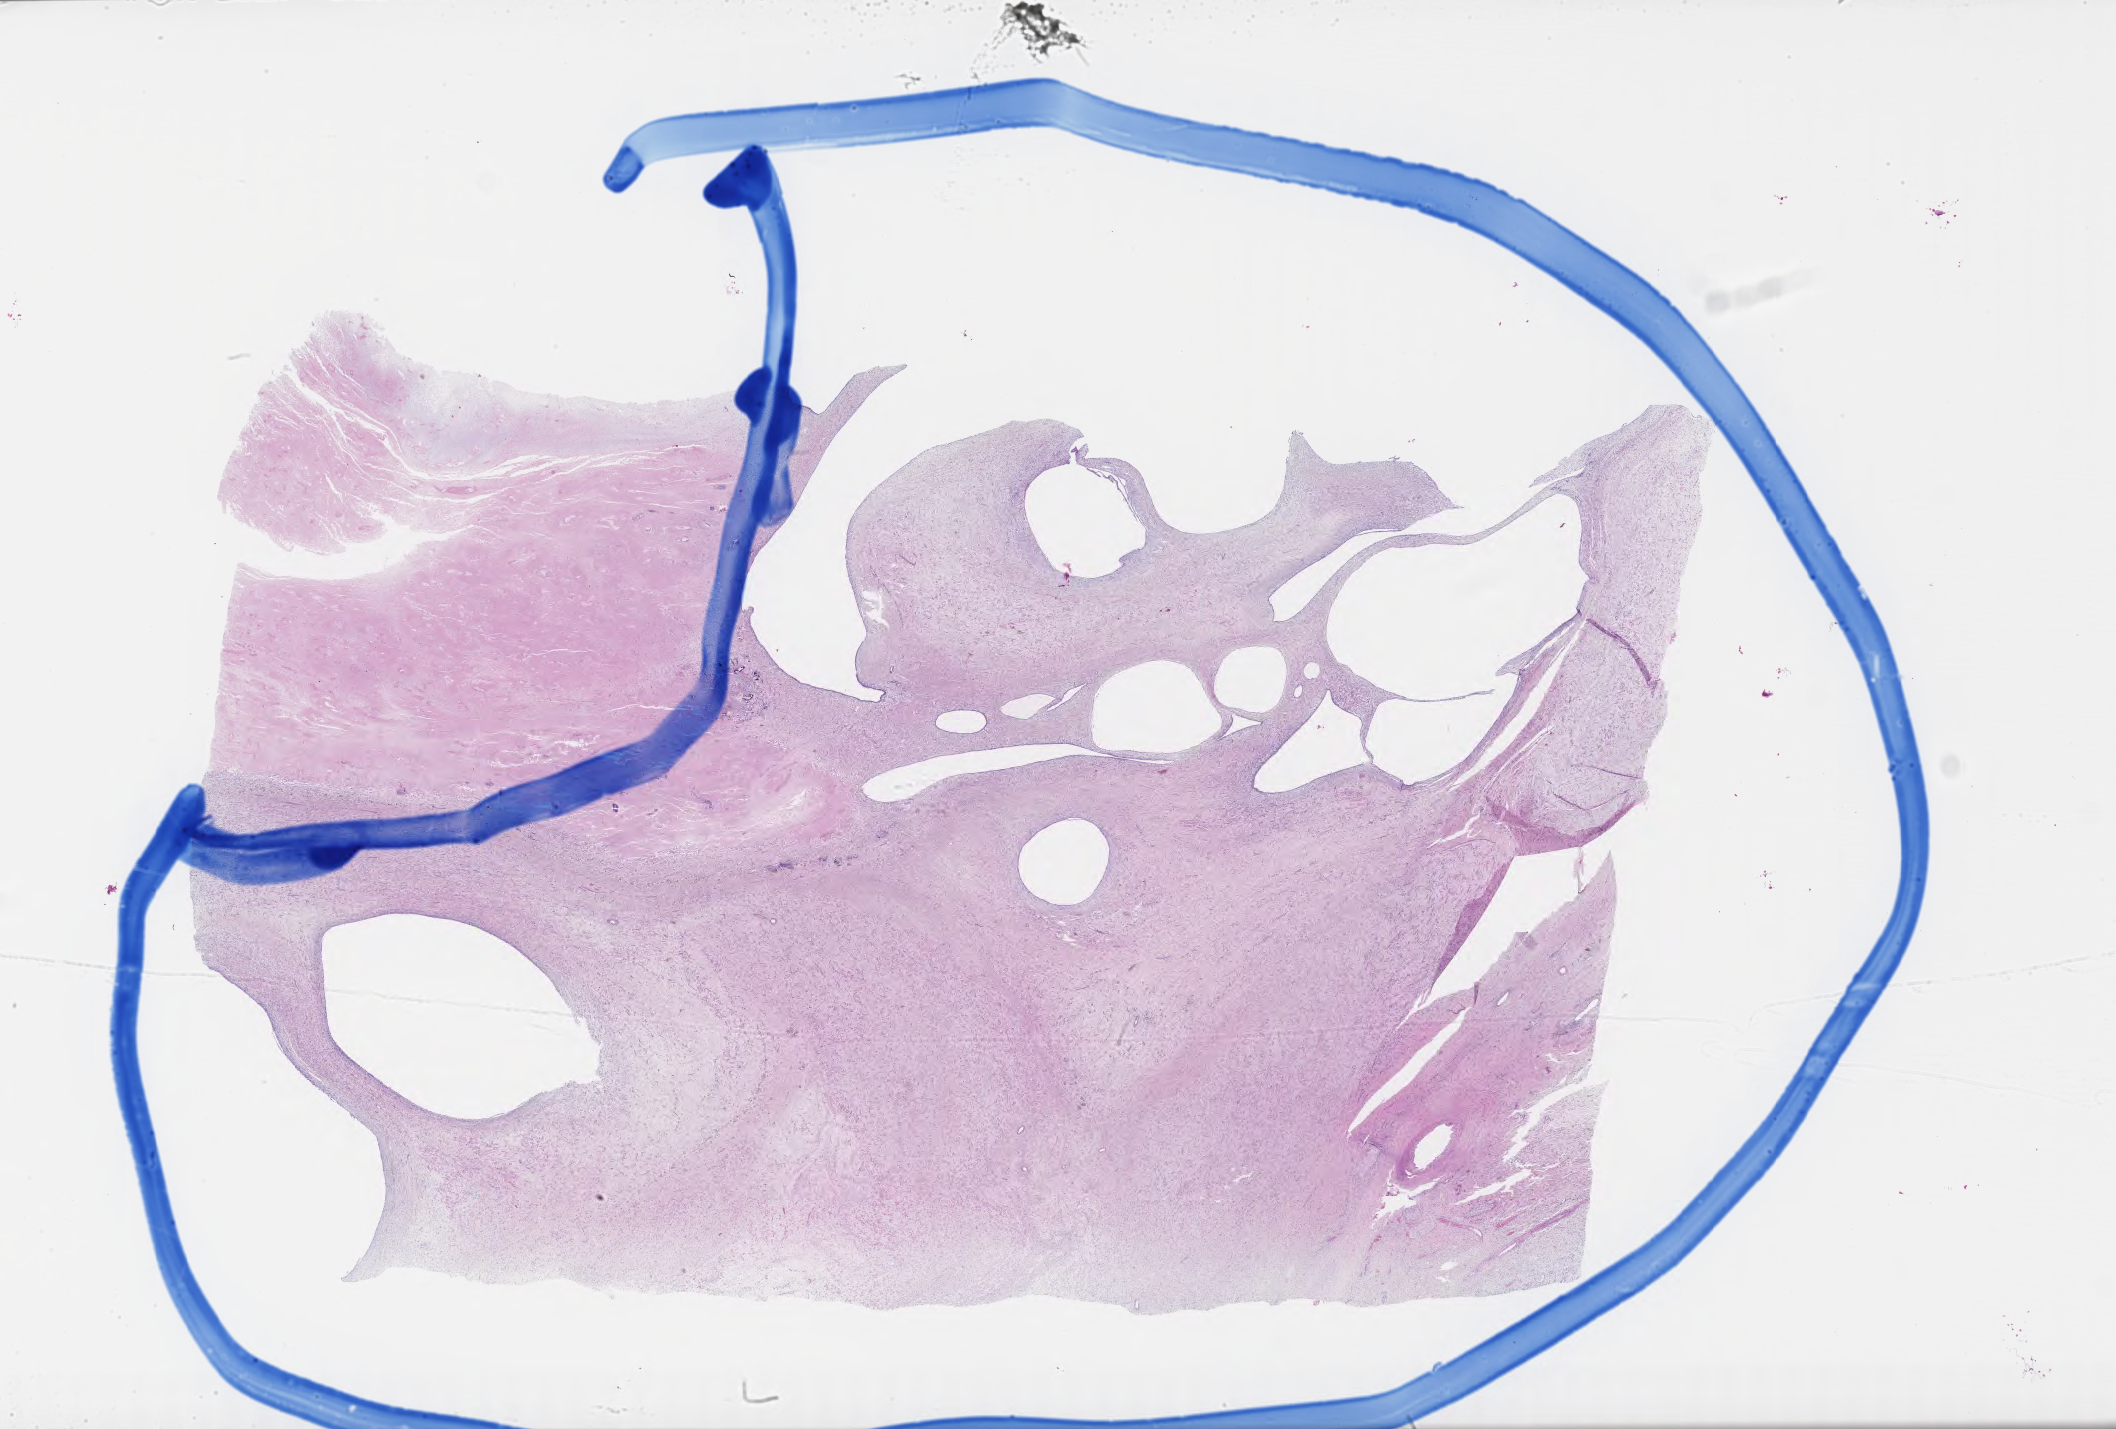
H&E whole-slide image — shown as a low-resolution overview of the whole scanned area (about 34.2 x 23.1 mm). FFPE section. Primary tumor. Anatomic site: kidney (left). Patient: male, age at initial diagnosis 1 years. Pathologist review of this section (percent, as recorded): tumor cells 80%, tumor nuclei 90%, stromal cells 0%, necrosis 20%, normal cells 0%. Infiltration values recorded for this section: lymphocyte infiltration 0%, monocyte infiltration 0%, neutrophil infiltration 0%.
Histologic diagnosis: Nephroblastoma, NOS. Section: top of the tissue portion.